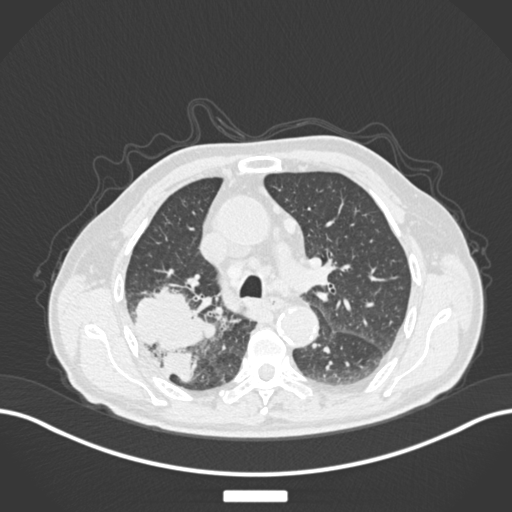
Chest CT, one axial slice. Slice 122 of 201 in the series (ordered by position). Reconstruction kernel B30f. Lung window (W 1500 / L -600 HU). 1 mm slice thickness. 512 × 512 image matrix, field of view 400 × 400 mm. Male patient, age 72 years. Case-level facts recorded for this patient, not image findings: clinical TNM (as recorded): T3 N2 M0.
Structures marked on this image (bounding box drawn by a radiologist):
- lung tumour (recorded histology: adenocarcinoma): bounding box (x1, y1, x2, y2) in pixels: (134, 279, 213, 385)